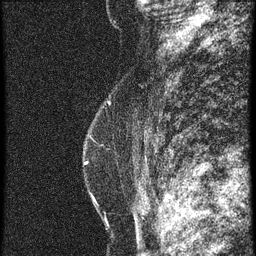
Breast MRI (dynamic contrast-enhanced), one sagittal slice. Position 39 of 60 along the scan axis. 3 images stored at this slice position (order not interpretable as contrast timing). 1.5 T. TE 4.2 ms, TR 20.4 ms. 256 × 256 image matrix, field of view 180 × 180 mm. Patient: female, 46 years. Case-level facts recorded for this patient, not image findings: setting: breast cancer imaged before/during neoadjuvant chemotherapy; receptor status: triple-negative.
Annotated regions visible in this slice (semi-automatic segmentation, software-assisted and operator-edited):
- analysis volume of interest (the breast-tissue region the enhancement analysis was run in; not a lesion): bounding box (x1, y1, x2, y2) in pixels: (69, 72, 142, 183)
- tumour enhancement mask (voxels above the 90 % enhancement threshold inside the analysis volume of interest): (86, 162, 88, 165)